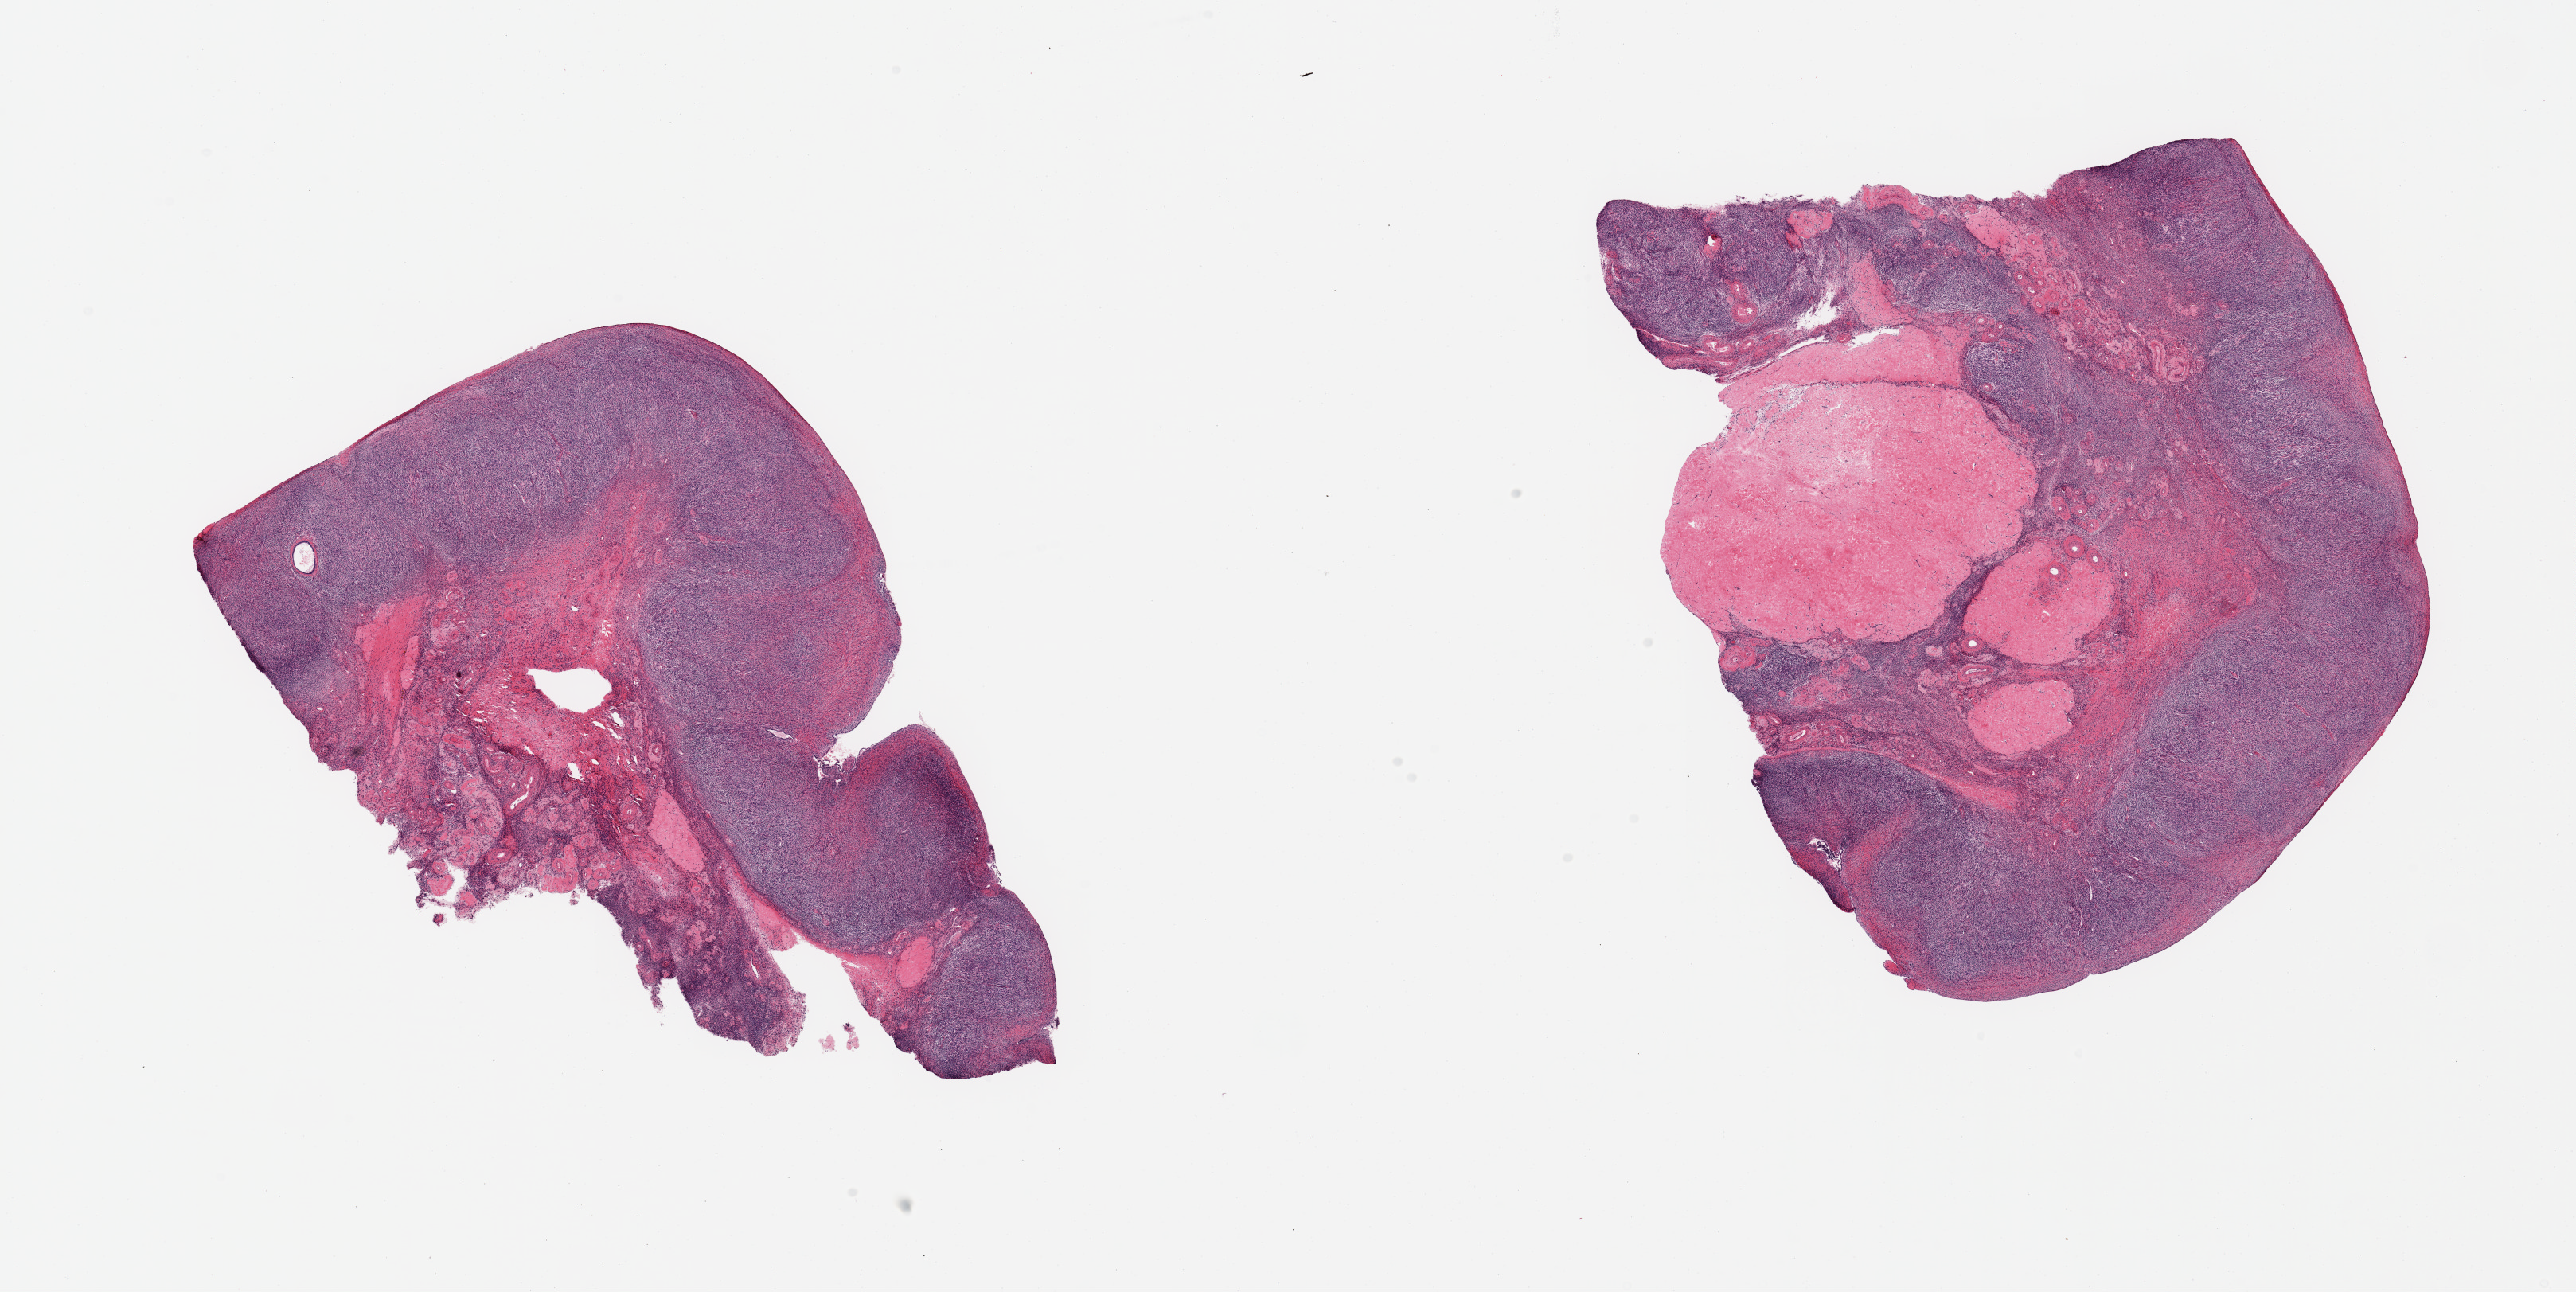
Digitized hematoxylin and eosin (H&E)-stained section — low-resolution overview of the scanned area, about 25.6 x 12.8 mm (slide scanned at 20x), PAXgene-fixed, paraffin-embedded tissue, section of ovary (target tissue), tissue donor sample. Donor: female.
Pathologist's review note for this sample: 2 pieces: 1 has corpora albicantia occupying 25% space; other has fibrovascular core occupying 30%.